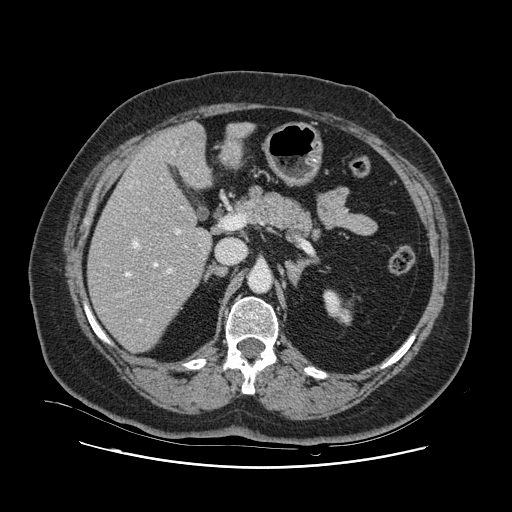
Contrast-enhanced abdominal CT, one axial slice. Position 58 of 132 along the scan axis. Intravenous contrast given. Soft-tissue window (W 400 / L 40 HU). 2.5 mm slice thickness. 512 × 512 image matrix, field of view 391 × 391 mm. Female patient, age 73 years. From the clinical record (not read from this slice): diagnosis: colorectal cancer liver metastases, imaged before liver resection; multiple liver metastases: no; largest metastasis: 7 cm; disease in both lobes: no.
Structures marked on this image (expert manual segmentation):
- hepatic veins: bounding box (x1, y1, x2, y2) in pixels: (126, 151, 183, 322)
- liver: (89, 124, 248, 352)
- planned liver remnant (the part of the liver to remain after resection): (89, 148, 211, 352)
- portal vein (with intrahepatic branches): (167, 229, 187, 273)